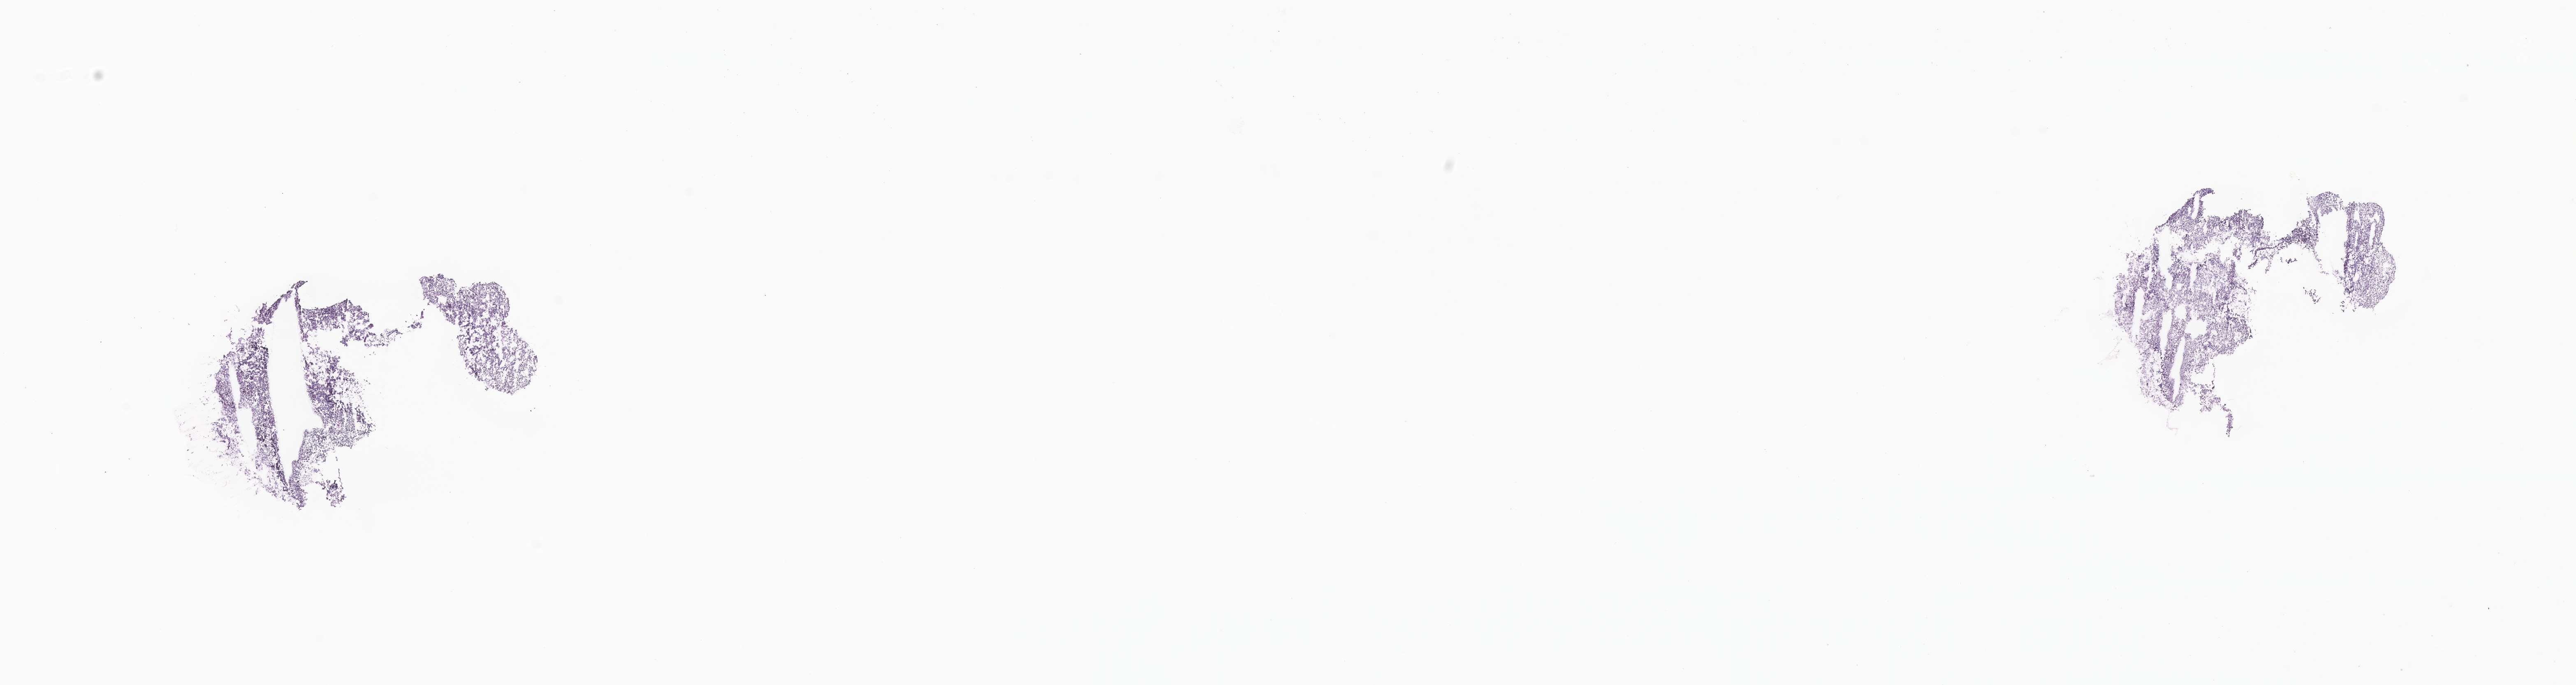
Whole-slide image, haematoxylin and eosin stain of tumor tissue from the brain — shown as a low-resolution overview of the whole scanned area (about 26.4 x 7.0 mm); frozen section (OCT-embedded). Patient male; age 35 months (2 years 11 months).
Diagnosis (ICD-O-3 morphology term): Large cell medulloblastoma.